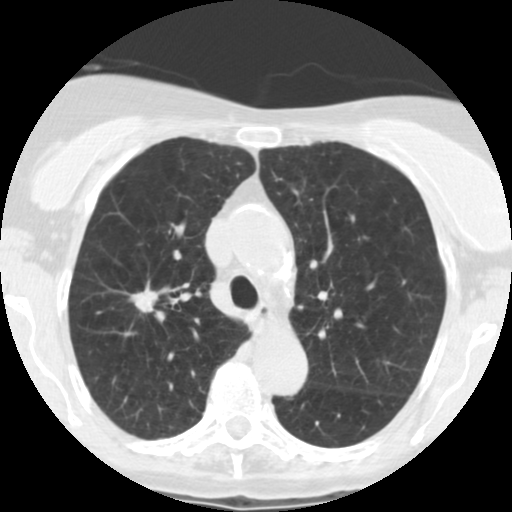
Low-dose screening chest CT, one axial slice; position 175 of 246 along the scan axis; reconstruction kernel STANDARD; 120 kVp; lung window (W 1500 / L -600 HU); 2.5 mm slice thickness; 512 × 512 image matrix.
Outlined on this slice (manually delineated by an expert):
- lesion 1 (tumor, upper lobe of right lung): bounding box <130,281,161,313> (left, top, right, bottom; pixels)